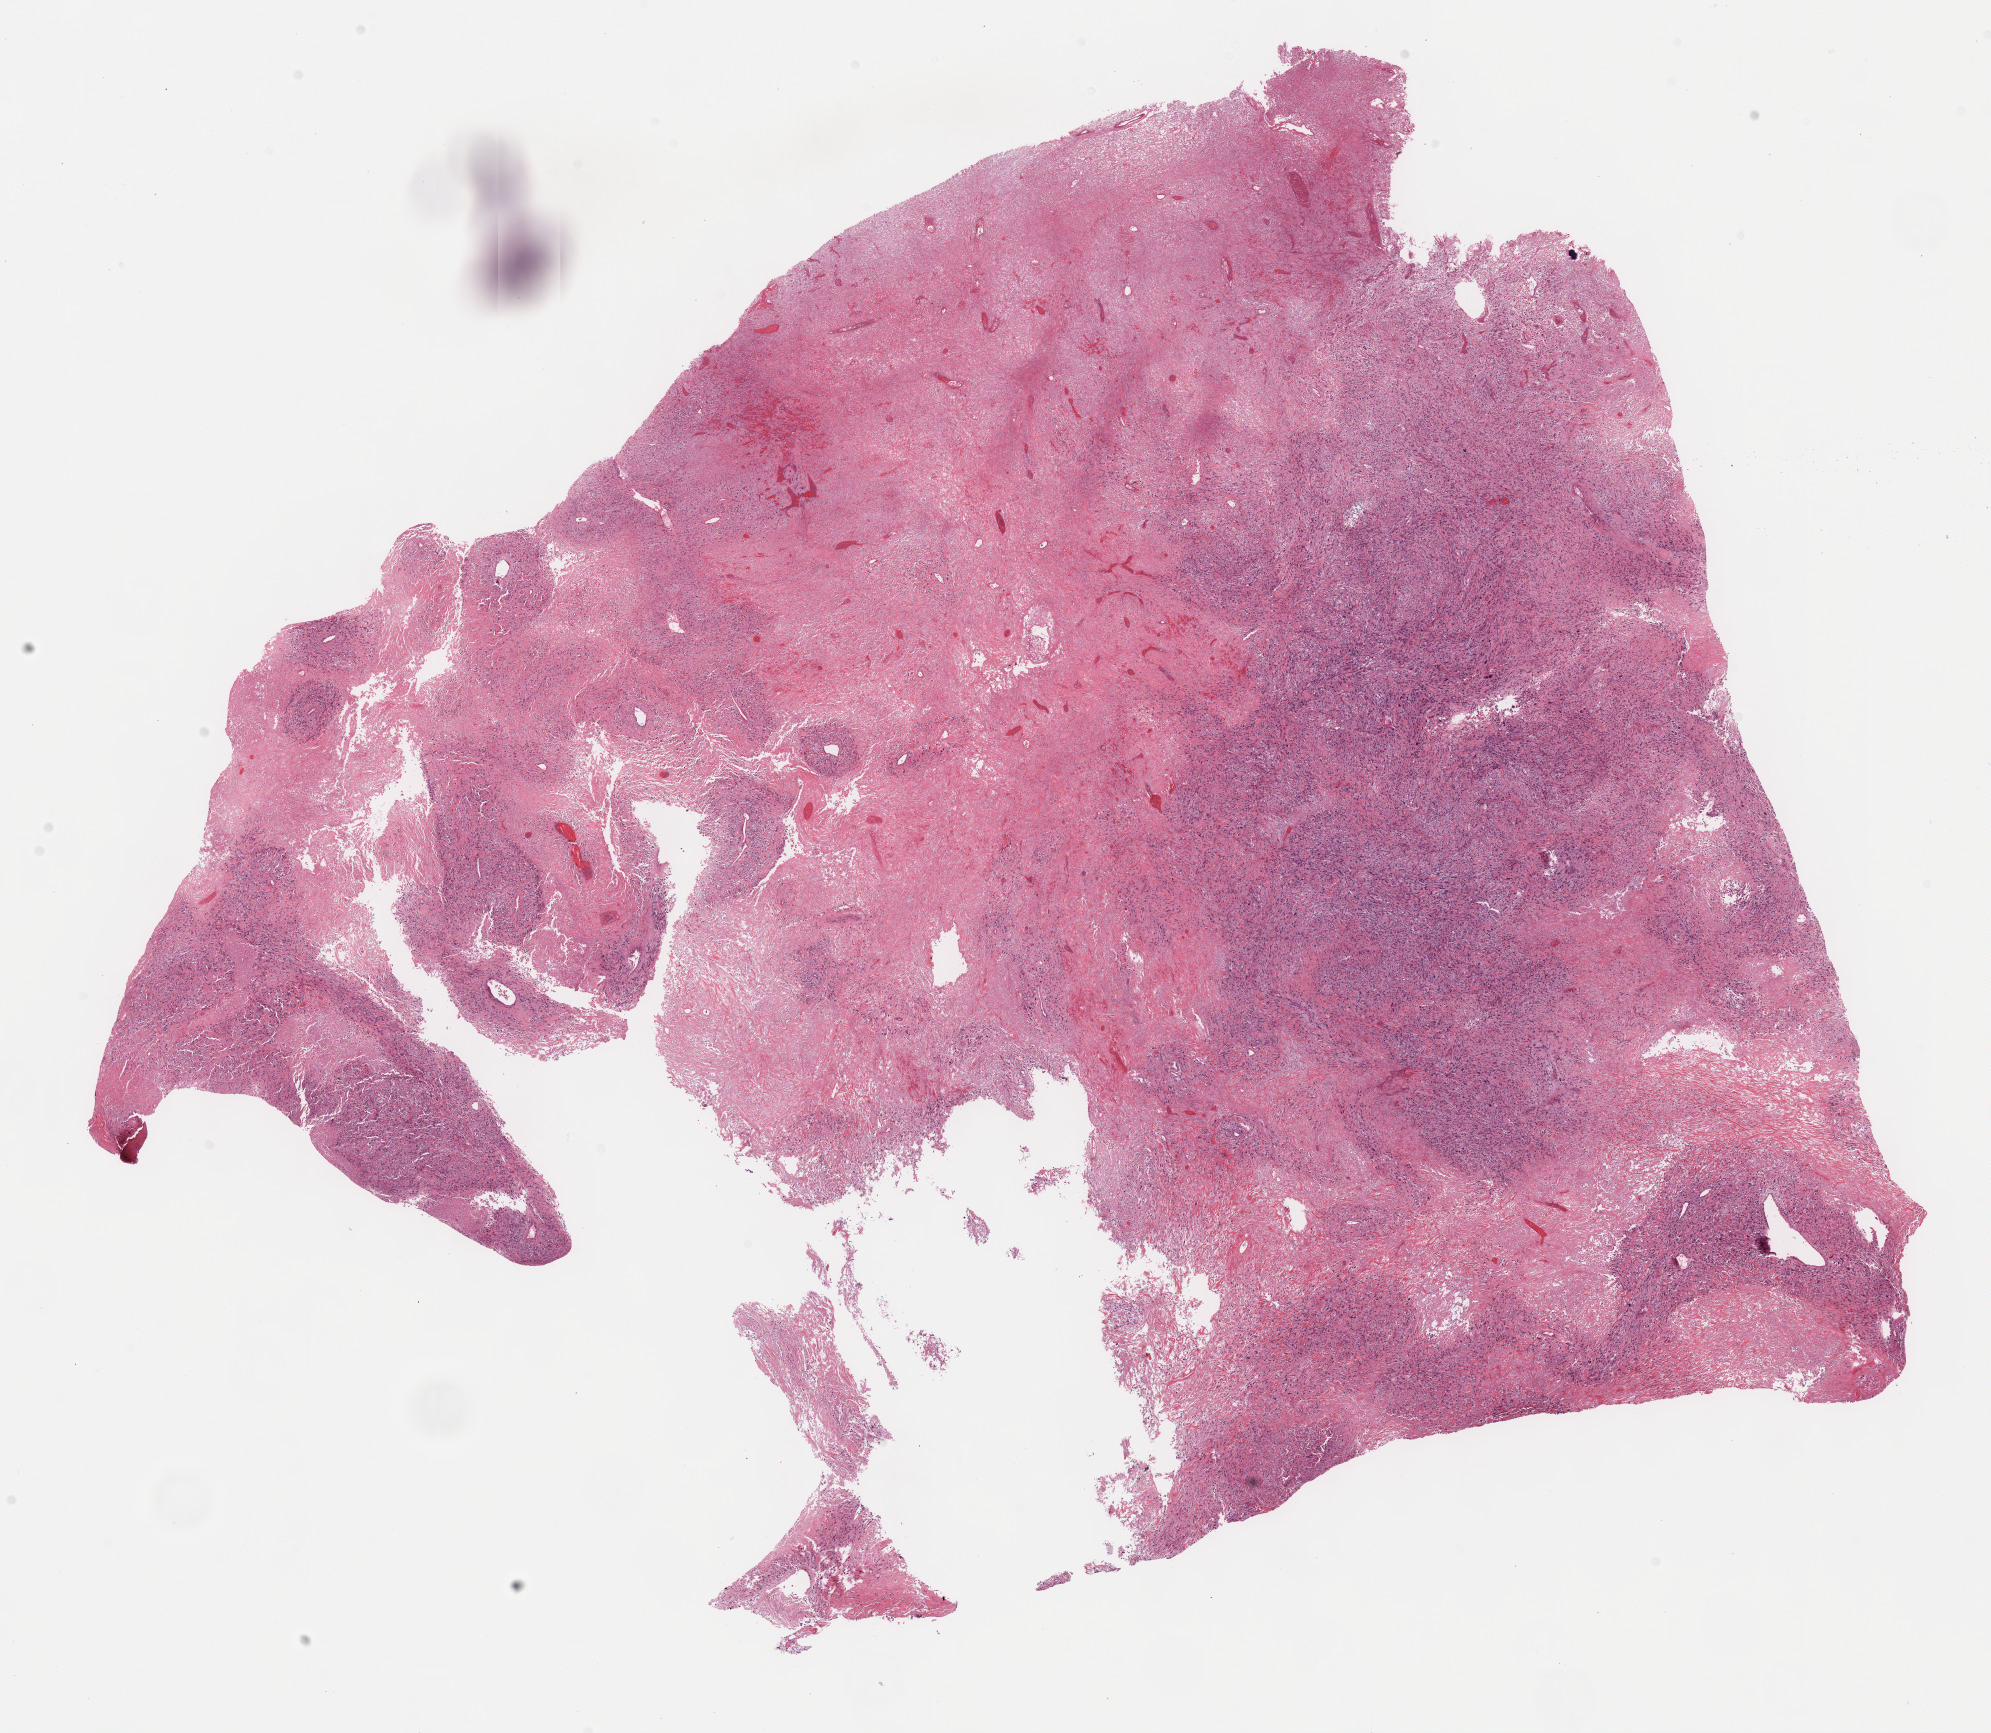
Hematoxylin and eosin (H&E) stained whole-slide image, a low-resolution overview of the entire scanned area, about 16.1 x 14.0 mm; formalin-fixed paraffin-embedded (FFPE) diagnostic section; connective, subcutaneous and other soft tissues, primary tumour sample. Patient: male, age at initial diagnosis 58 years.
Diagnosis: Malignant fibrous histiocytoma (connective, subcutaneous and other soft tissues of lower limb and hip).